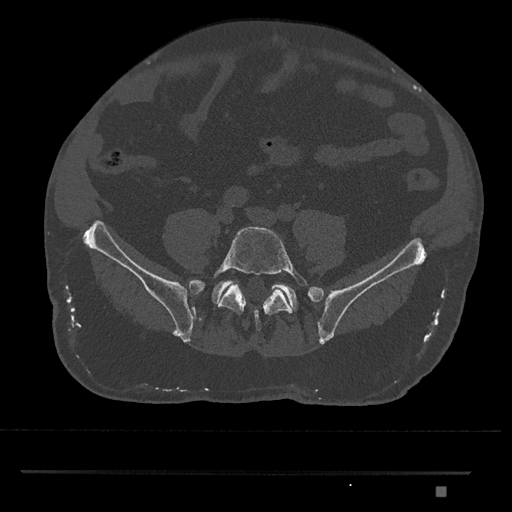
CT including the spine, one axial slice; slice 546 of 1134 in the series (ordered by position); reconstruction kernel Br40s/3; 120 kVp; bone window (W 1800 / L 400 HU); 0.5 mm slice thickness; 512 × 512 image matrix, field of view 429 × 429 mm. Male patient, age 65 years. Case-level facts recorded for this patient, not image findings: primary cancer: prostate.
Structures marked on this image (semi-automatic segmentation, software-assisted and operator-edited):
- L5 vertebra: box from (x=211, y=226) to (x=310, y=331) px